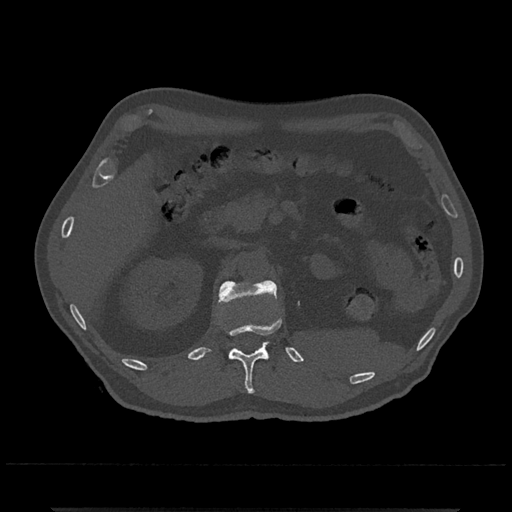
CT including the spine, one axial slice; reconstruction kernel Br40s/3; 120 kVp; bone window (W 1800 / L 400 HU); 0.5 mm slice thickness; 512 × 512 image matrix, field of view 393 × 393 mm. Male patient, age 67 years. Case-level facts recorded for this patient, not image findings: primary cancer: prostate.
Outlined on this slice (semi-automatically segmented with operator editing):
- L1 vertebra: bounding box (x1, y1, x2, y2) in pixels: (218, 280, 277, 358)
- T12 vertebra: (229, 319, 281, 394)